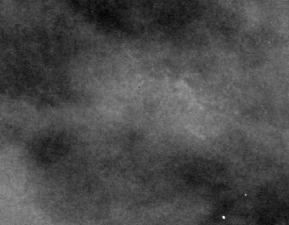
Region of interest cut from a scanned film mammogram (one marked finding); left breast; MLO view; BI-RADS breast density category 3 (scale 1–4).
Calcifications, morphology punctate / amorphous, distribution clustered; BI-RADS assessment category 4; pathology result (as recorded, not read from the image): benign.